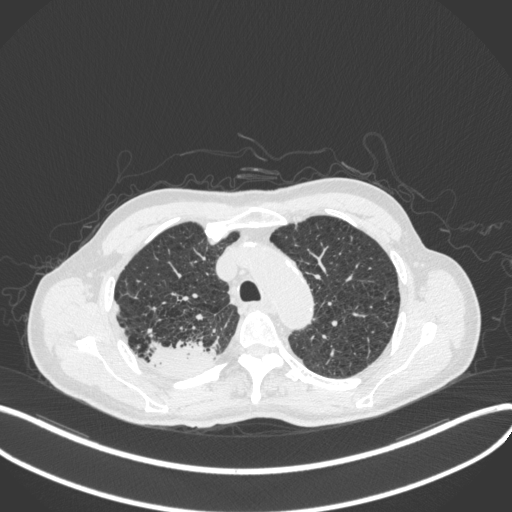
Chest CT, one axial slice; slice 338 of 423 in the series (ordered by position); reconstruction kernel B31f; 120 kVp; lung window (W 1500 / L -600 HU); 512 × 512 image matrix, field of view 400 × 400 mm. Patient: male, 79 years. Case-level facts recorded for this patient, not image findings: clinical TNM (as recorded): T3 N0 M0.
Outlined on this slice (bounding box drawn by a radiologist):
- lung tumour (recorded histology: adenocarcinoma): bounding box [x1, y1, x2, y2] px = [144, 334, 217, 377]